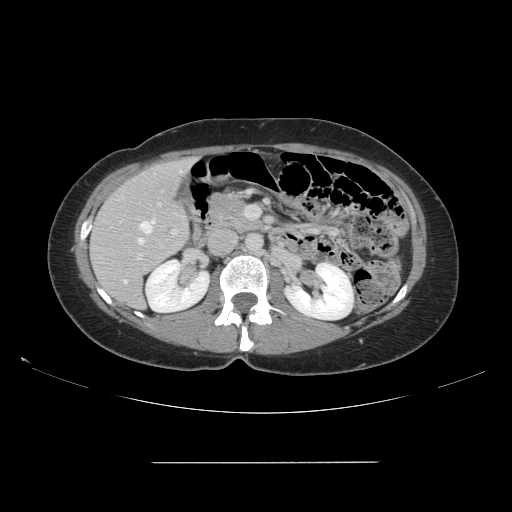
Contrast-enhanced abdominal CT, one axial slice. Slice 75 of 151 in the series (ordered by position). 120 kVp. Intravenous contrast given. Soft-tissue window (W 400 / L 40 HU). 2.5 mm slice thickness. 512 × 512 image matrix, field of view 421 × 421 mm. Female patient, age 46 years. From the clinical record (not read from this slice): diagnosis: colorectal cancer liver metastases, imaged before liver resection; multiple liver metastases: yes; largest metastasis: 3 cm; disease in both lobes: yes.
Annotated regions visible in this slice (outlined manually by an expert reader):
- hepatic veins: box from (x=137, y=220) to (x=155, y=245) px
- liver: (x=92, y=160)–(x=193, y=308)
- planned liver remnant (the part of the liver to remain after resection): (x=93, y=160)–(x=192, y=309)
- portal vein (with intrahepatic branches): (x=135, y=202)–(x=178, y=260)